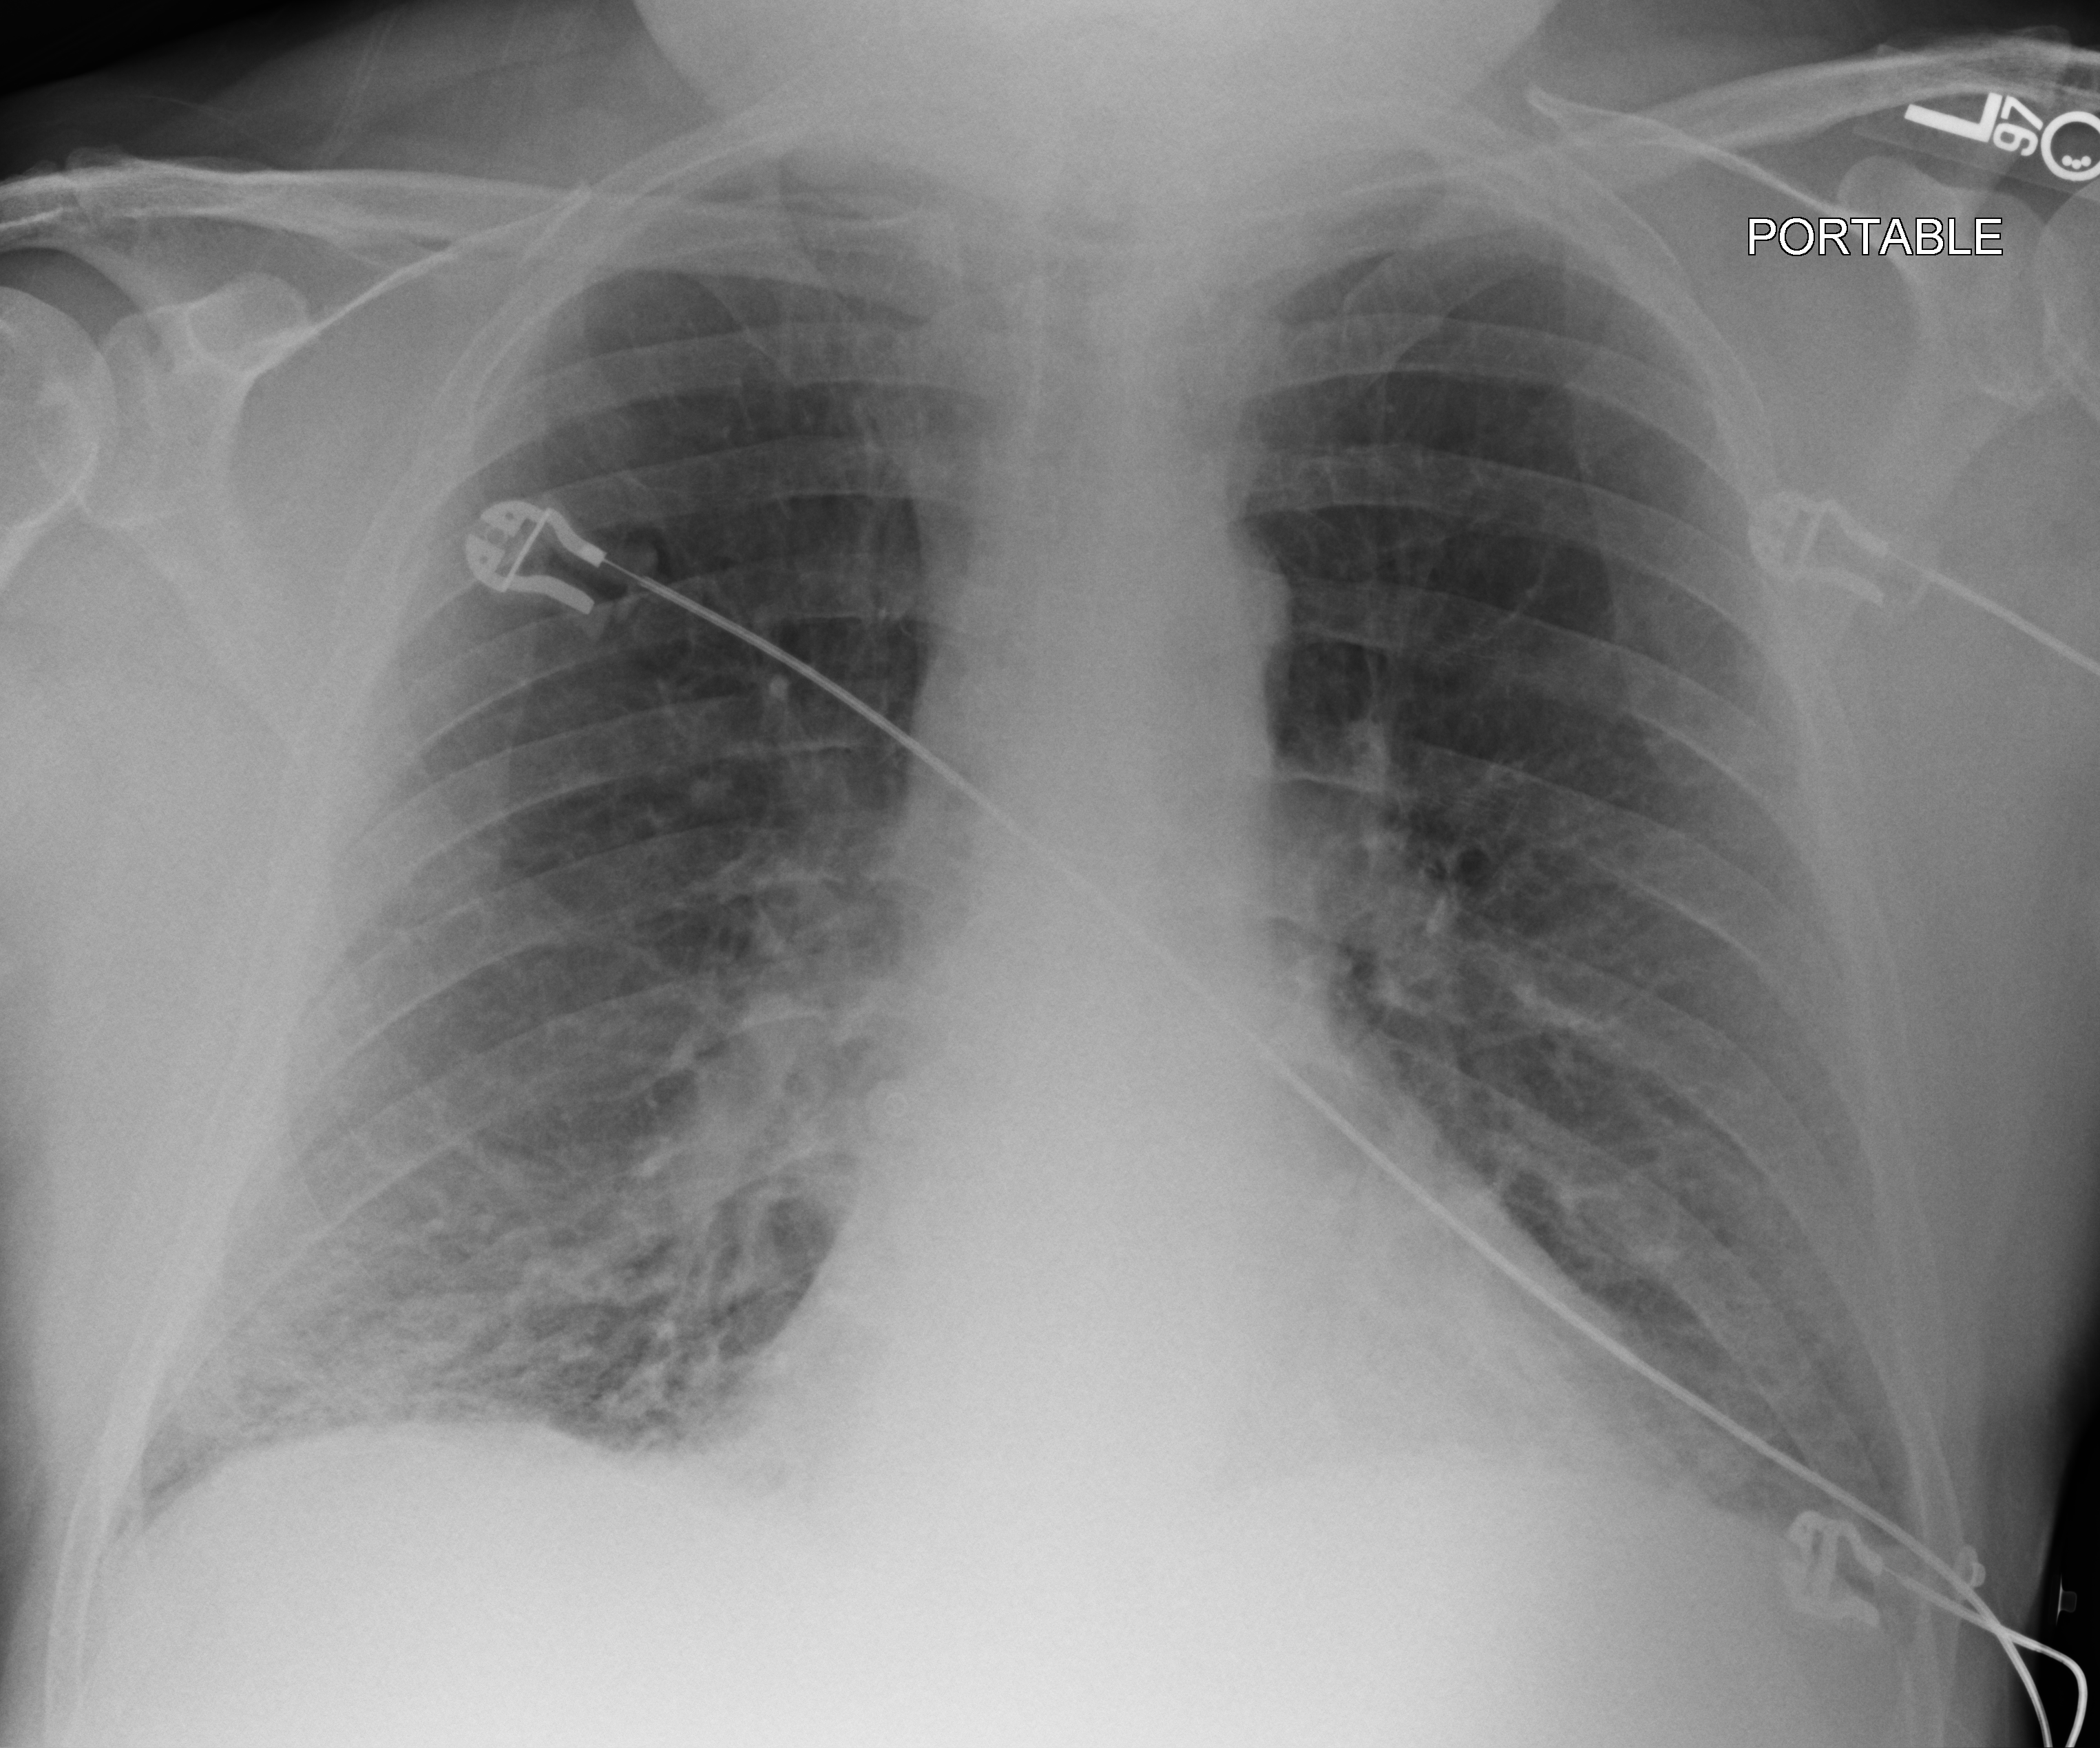
Chest X-ray (portable), anteroposterior (AP) projection. Patient hospitalised with COVID-19, aged 18–59 years.
From the hospital-stay record, not from the radiograph (when in the stay this image was taken is not recorded): mechanically ventilated during this hospital stay: no; admitted to intensive care during this hospital stay: yes.